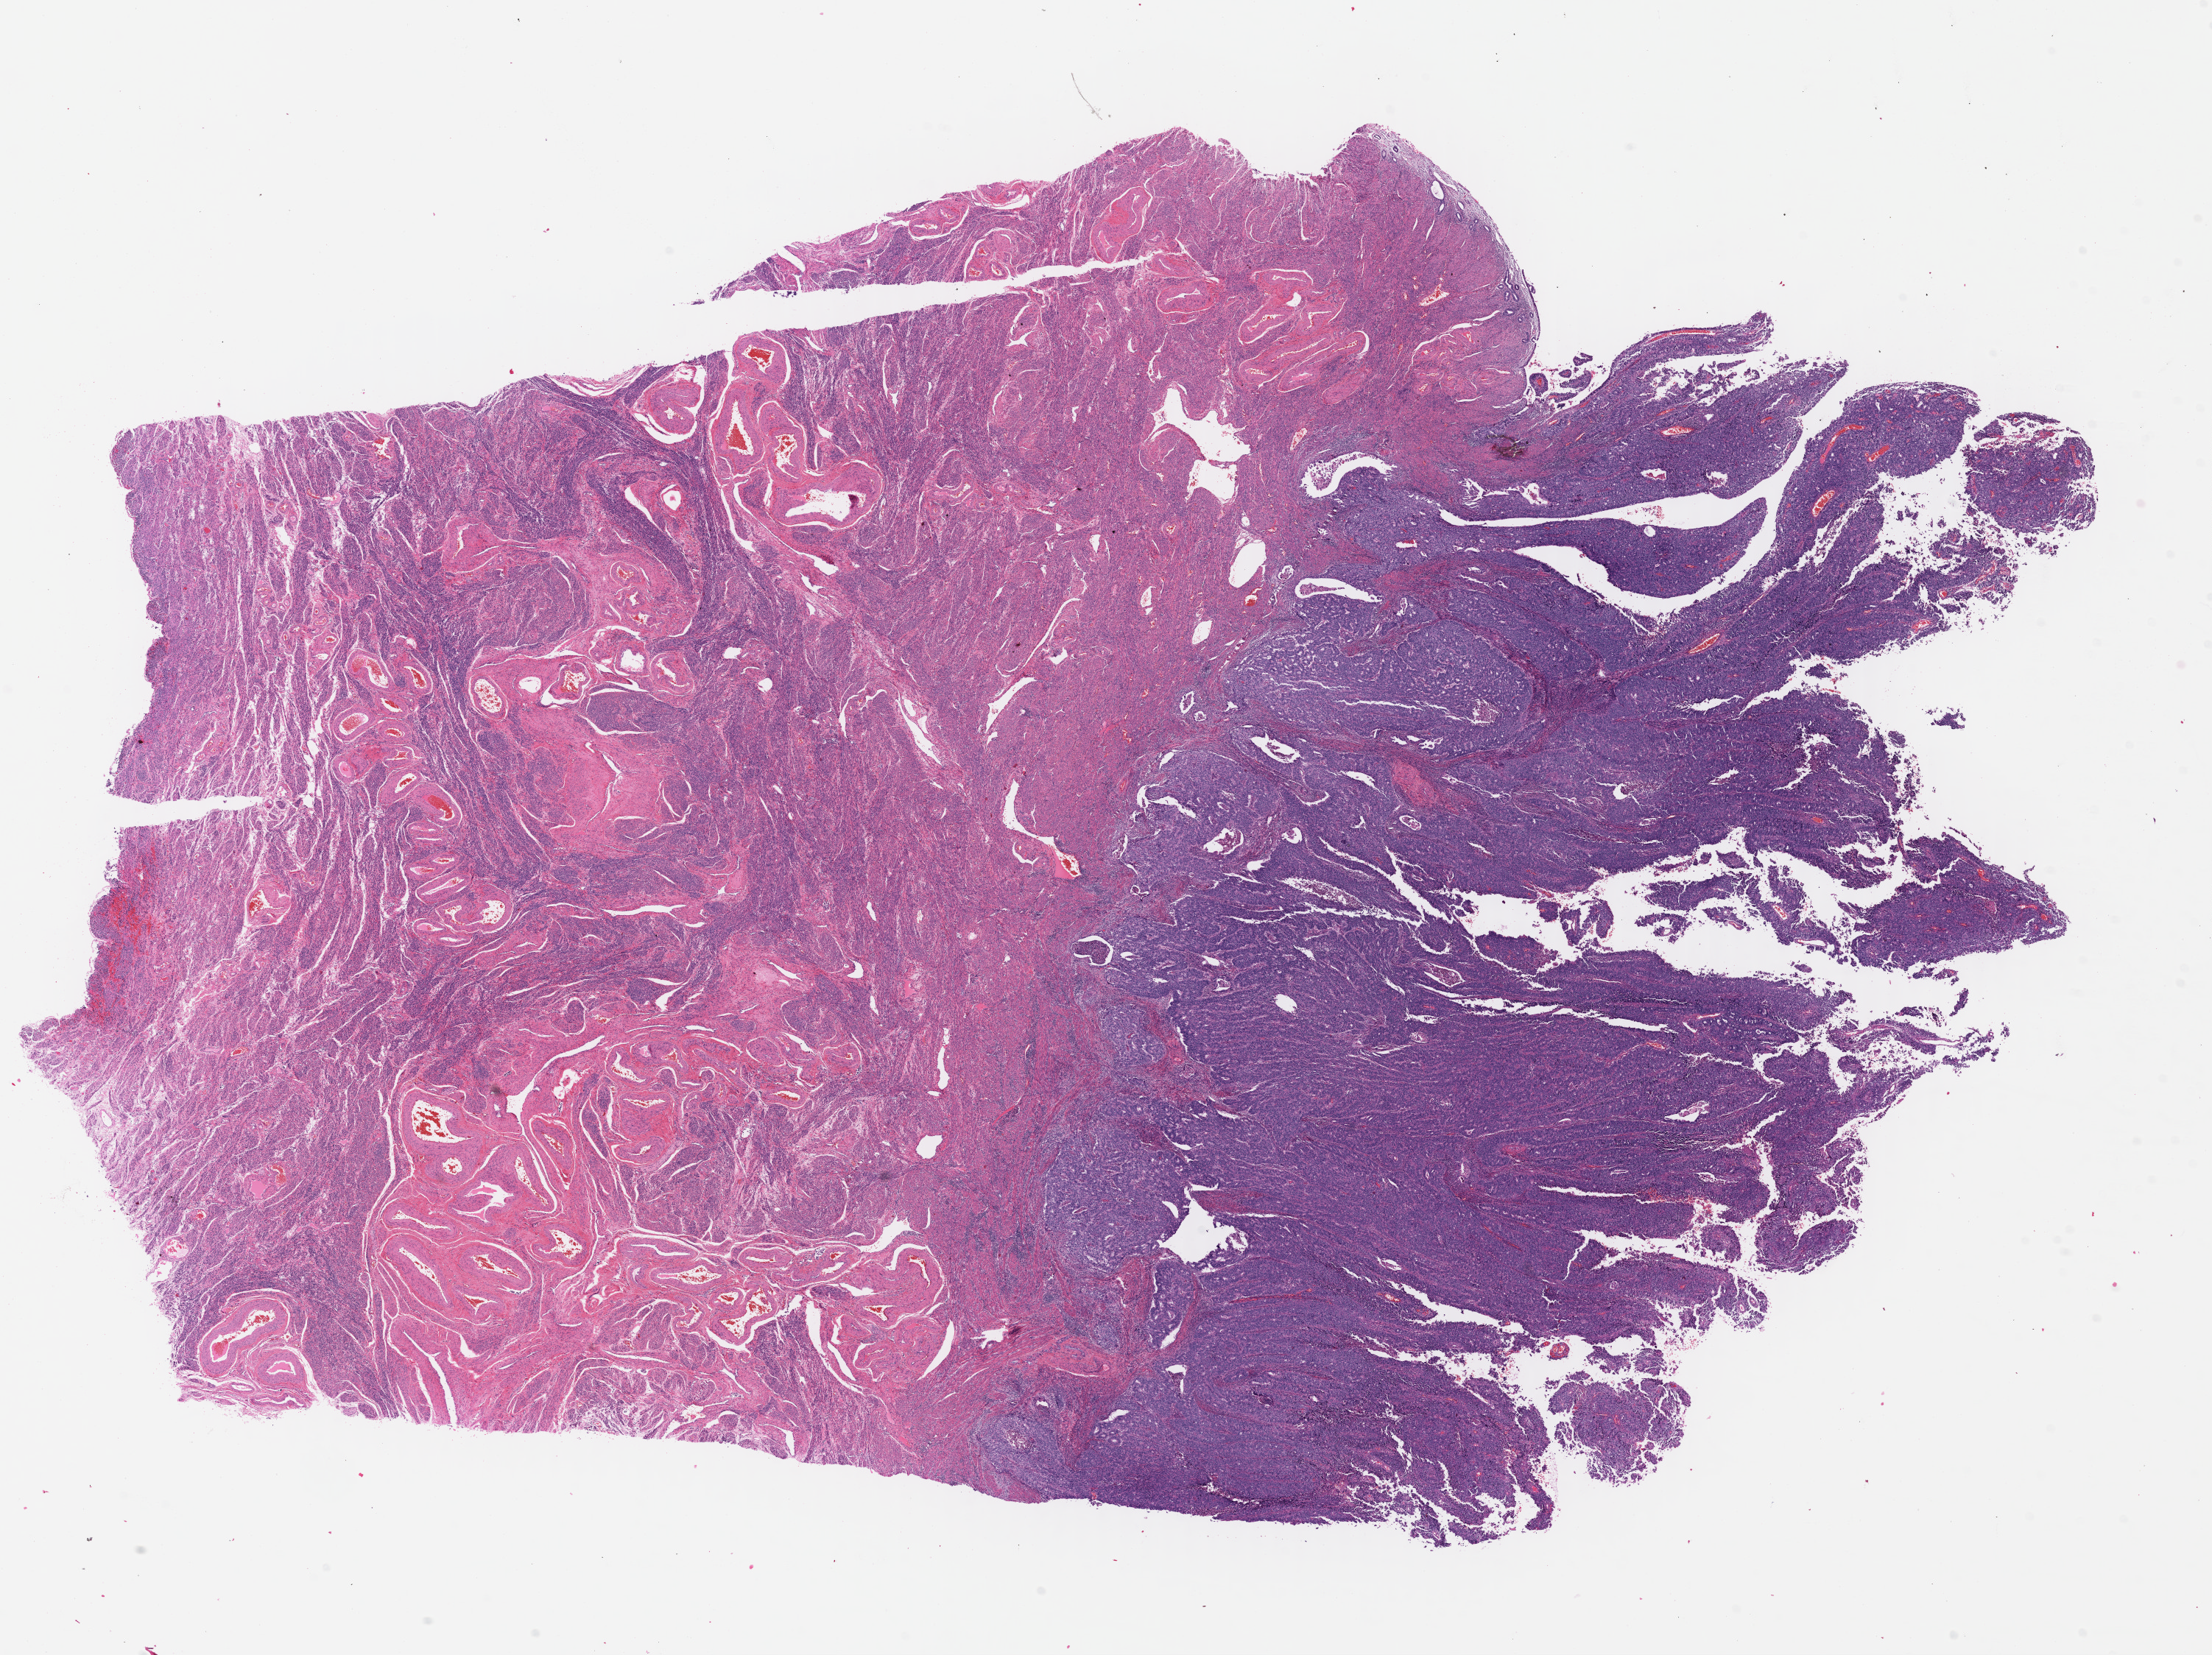
H&E-stained whole-slide image — shown as a low-resolution overview of the whole scanned area (about 23.6 x 17.7 mm, from a 40x scan). Formalin-fixed paraffin-embedded (FFPE) diagnostic section. Sample: primary tumour, uterus. Female patient; age at initial diagnosis 62 years. Histologic grade: G3 (poorly differentiated).
Histologic diagnosis: Endometrioid adenocarcinoma, NOS (endometrium). FIGO stage: IB.